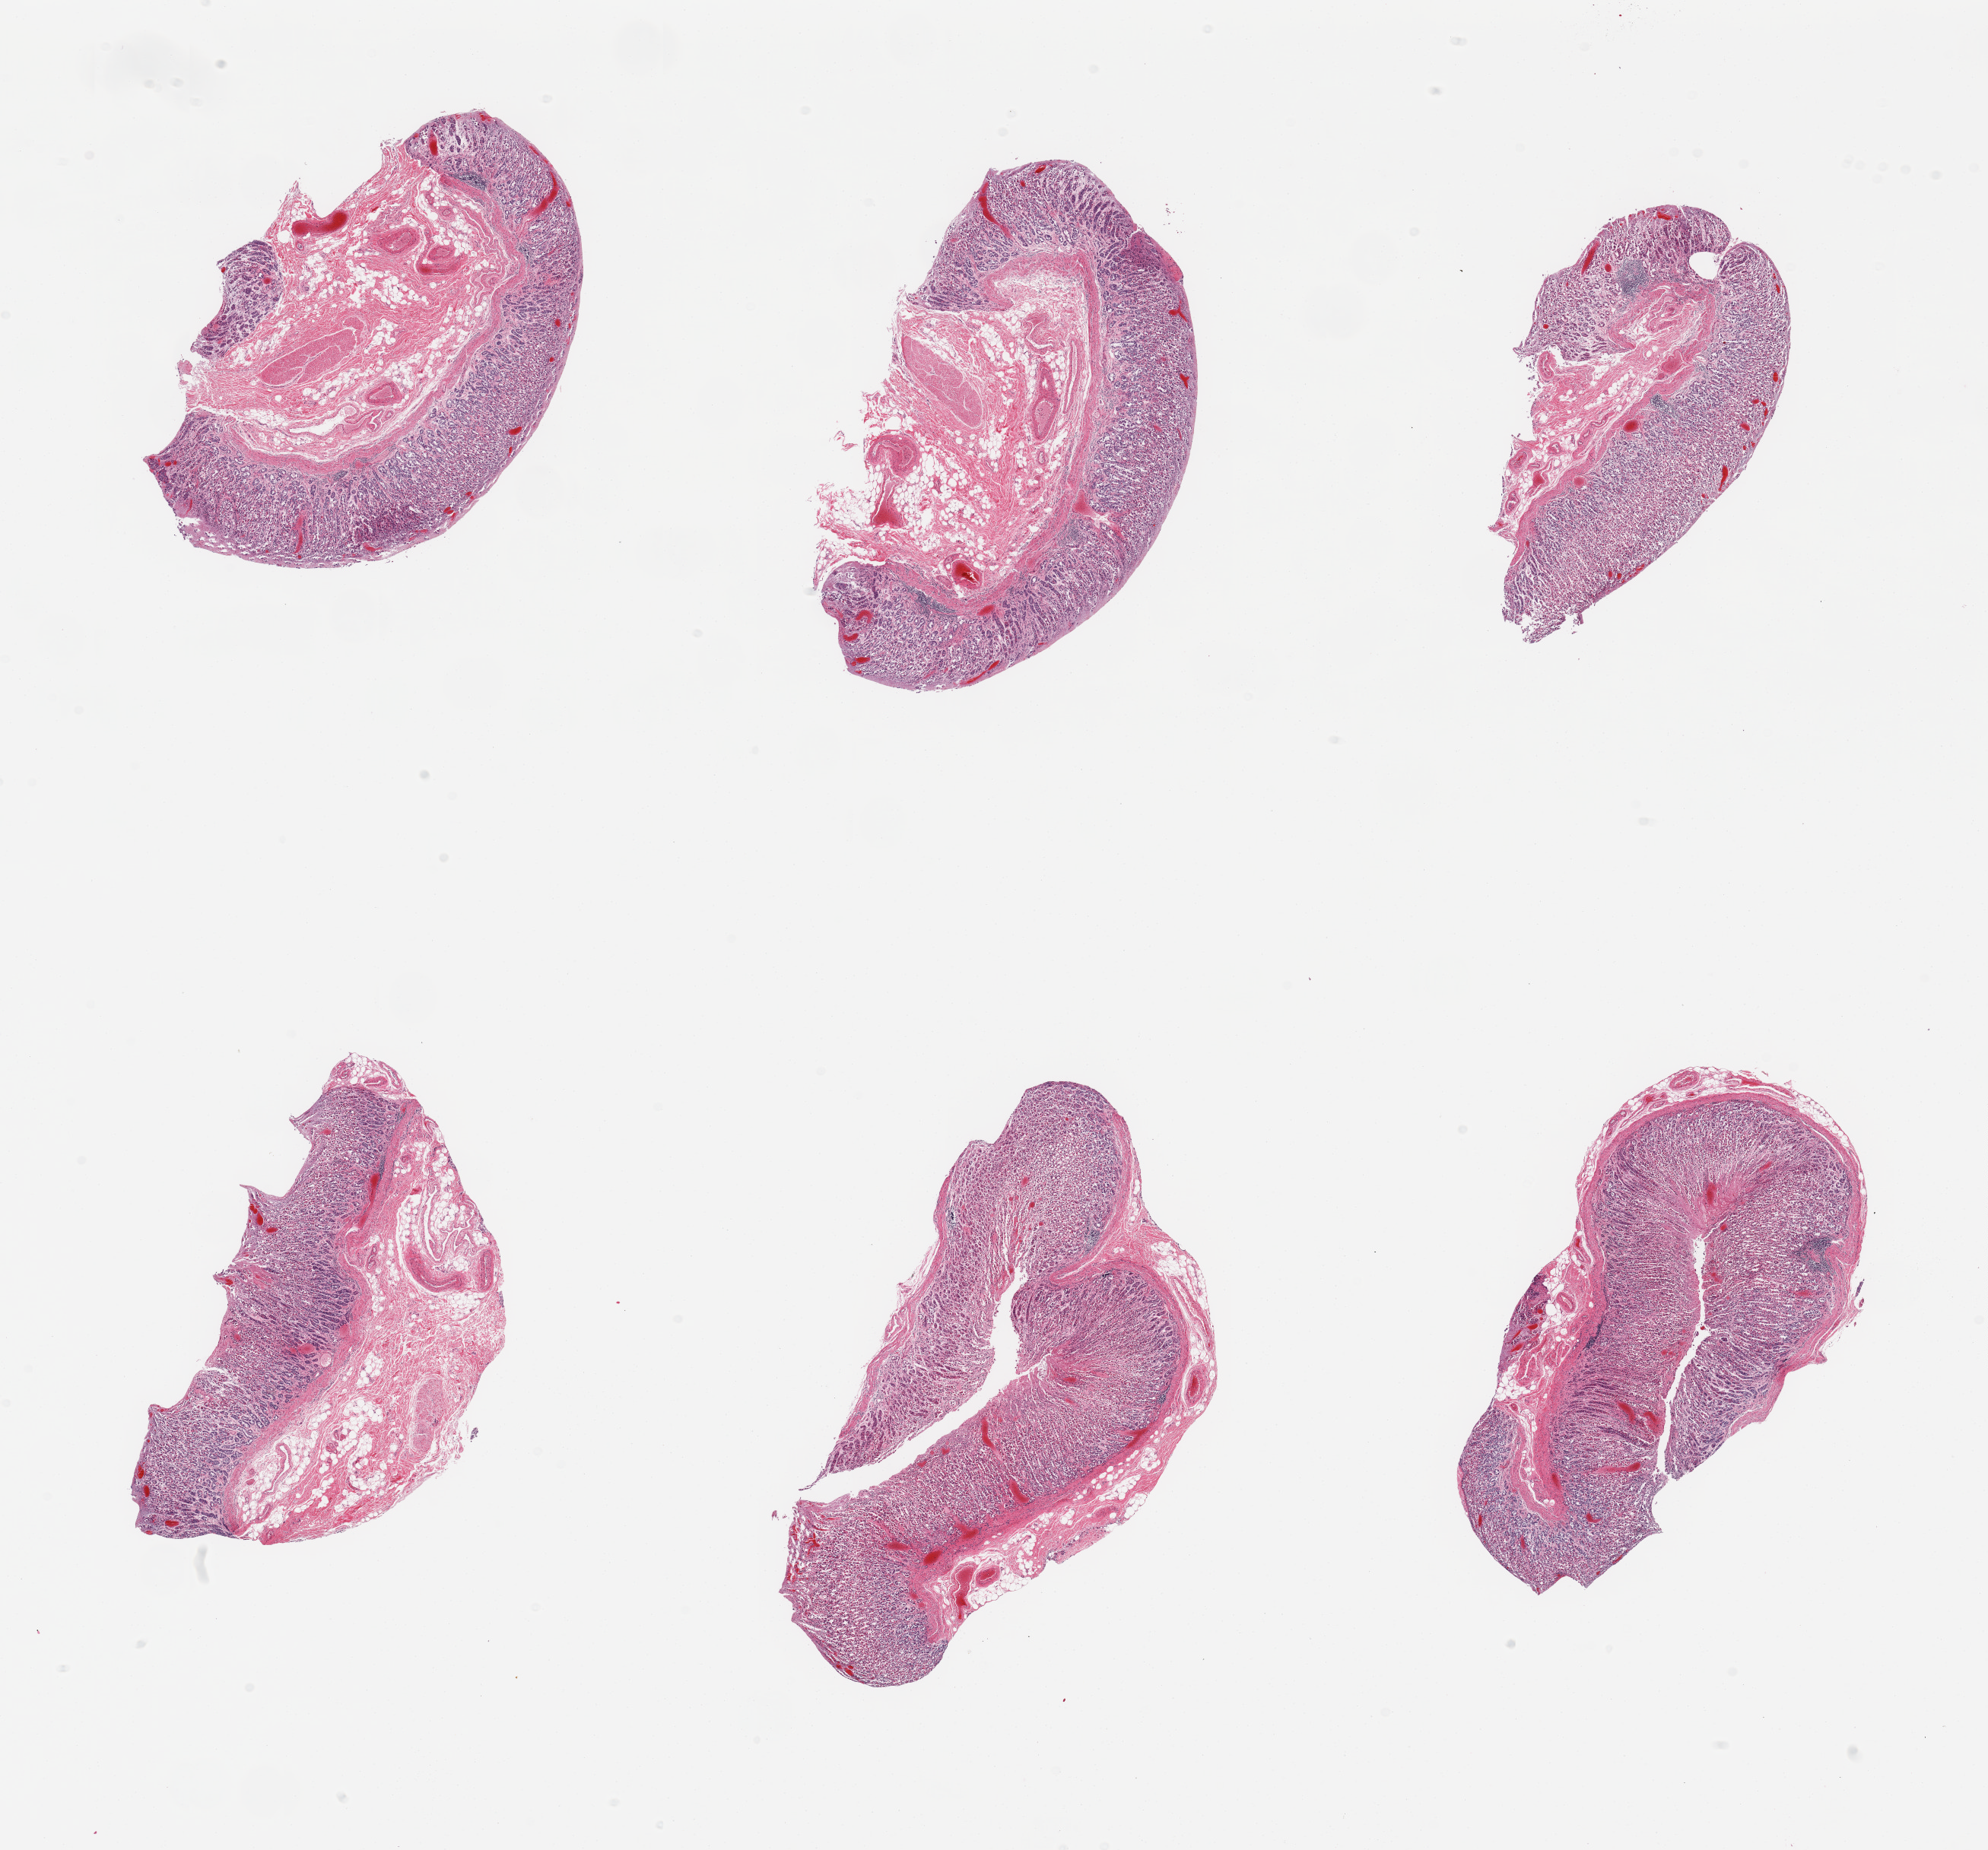
Whole-slide image, haematoxylin and eosin stain — whole scanned area (about 20.7 x 19.2 mm) shown as a low-resolution overview; PAXgene-fixed paraffin-embedded (PFPE) section; target tissue: stomach; tissue donor sample. Donor: male.
Review note (as recorded): 6 pieces, mucosa up to ~1mm, moderately advanced autolysis.